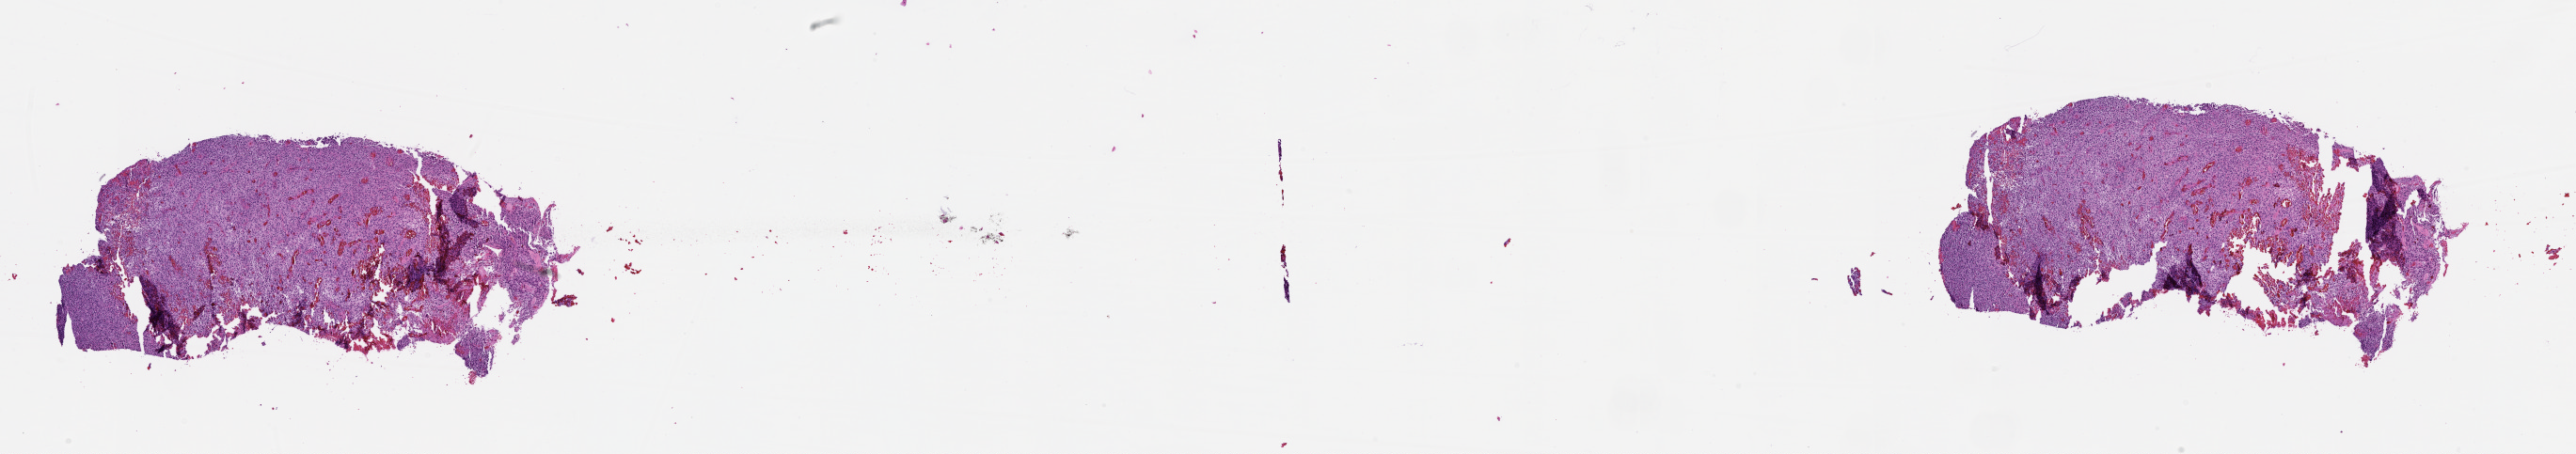
Digitized Hematoxylin and eosin (H&E) stained tissue section (whole slide) — low-resolution overview of the scanned area, about 22.0 x 3.9 mm (from a 20x scan), tumour tissue sample, sampled site: brain. 71-year-old female patient. Composition of this section per pathologist review: tumour nuclei 85%, necrosis 5%.
• diagnosis: Glioblastoma
• primary tumour site (as recorded): frontal lobe